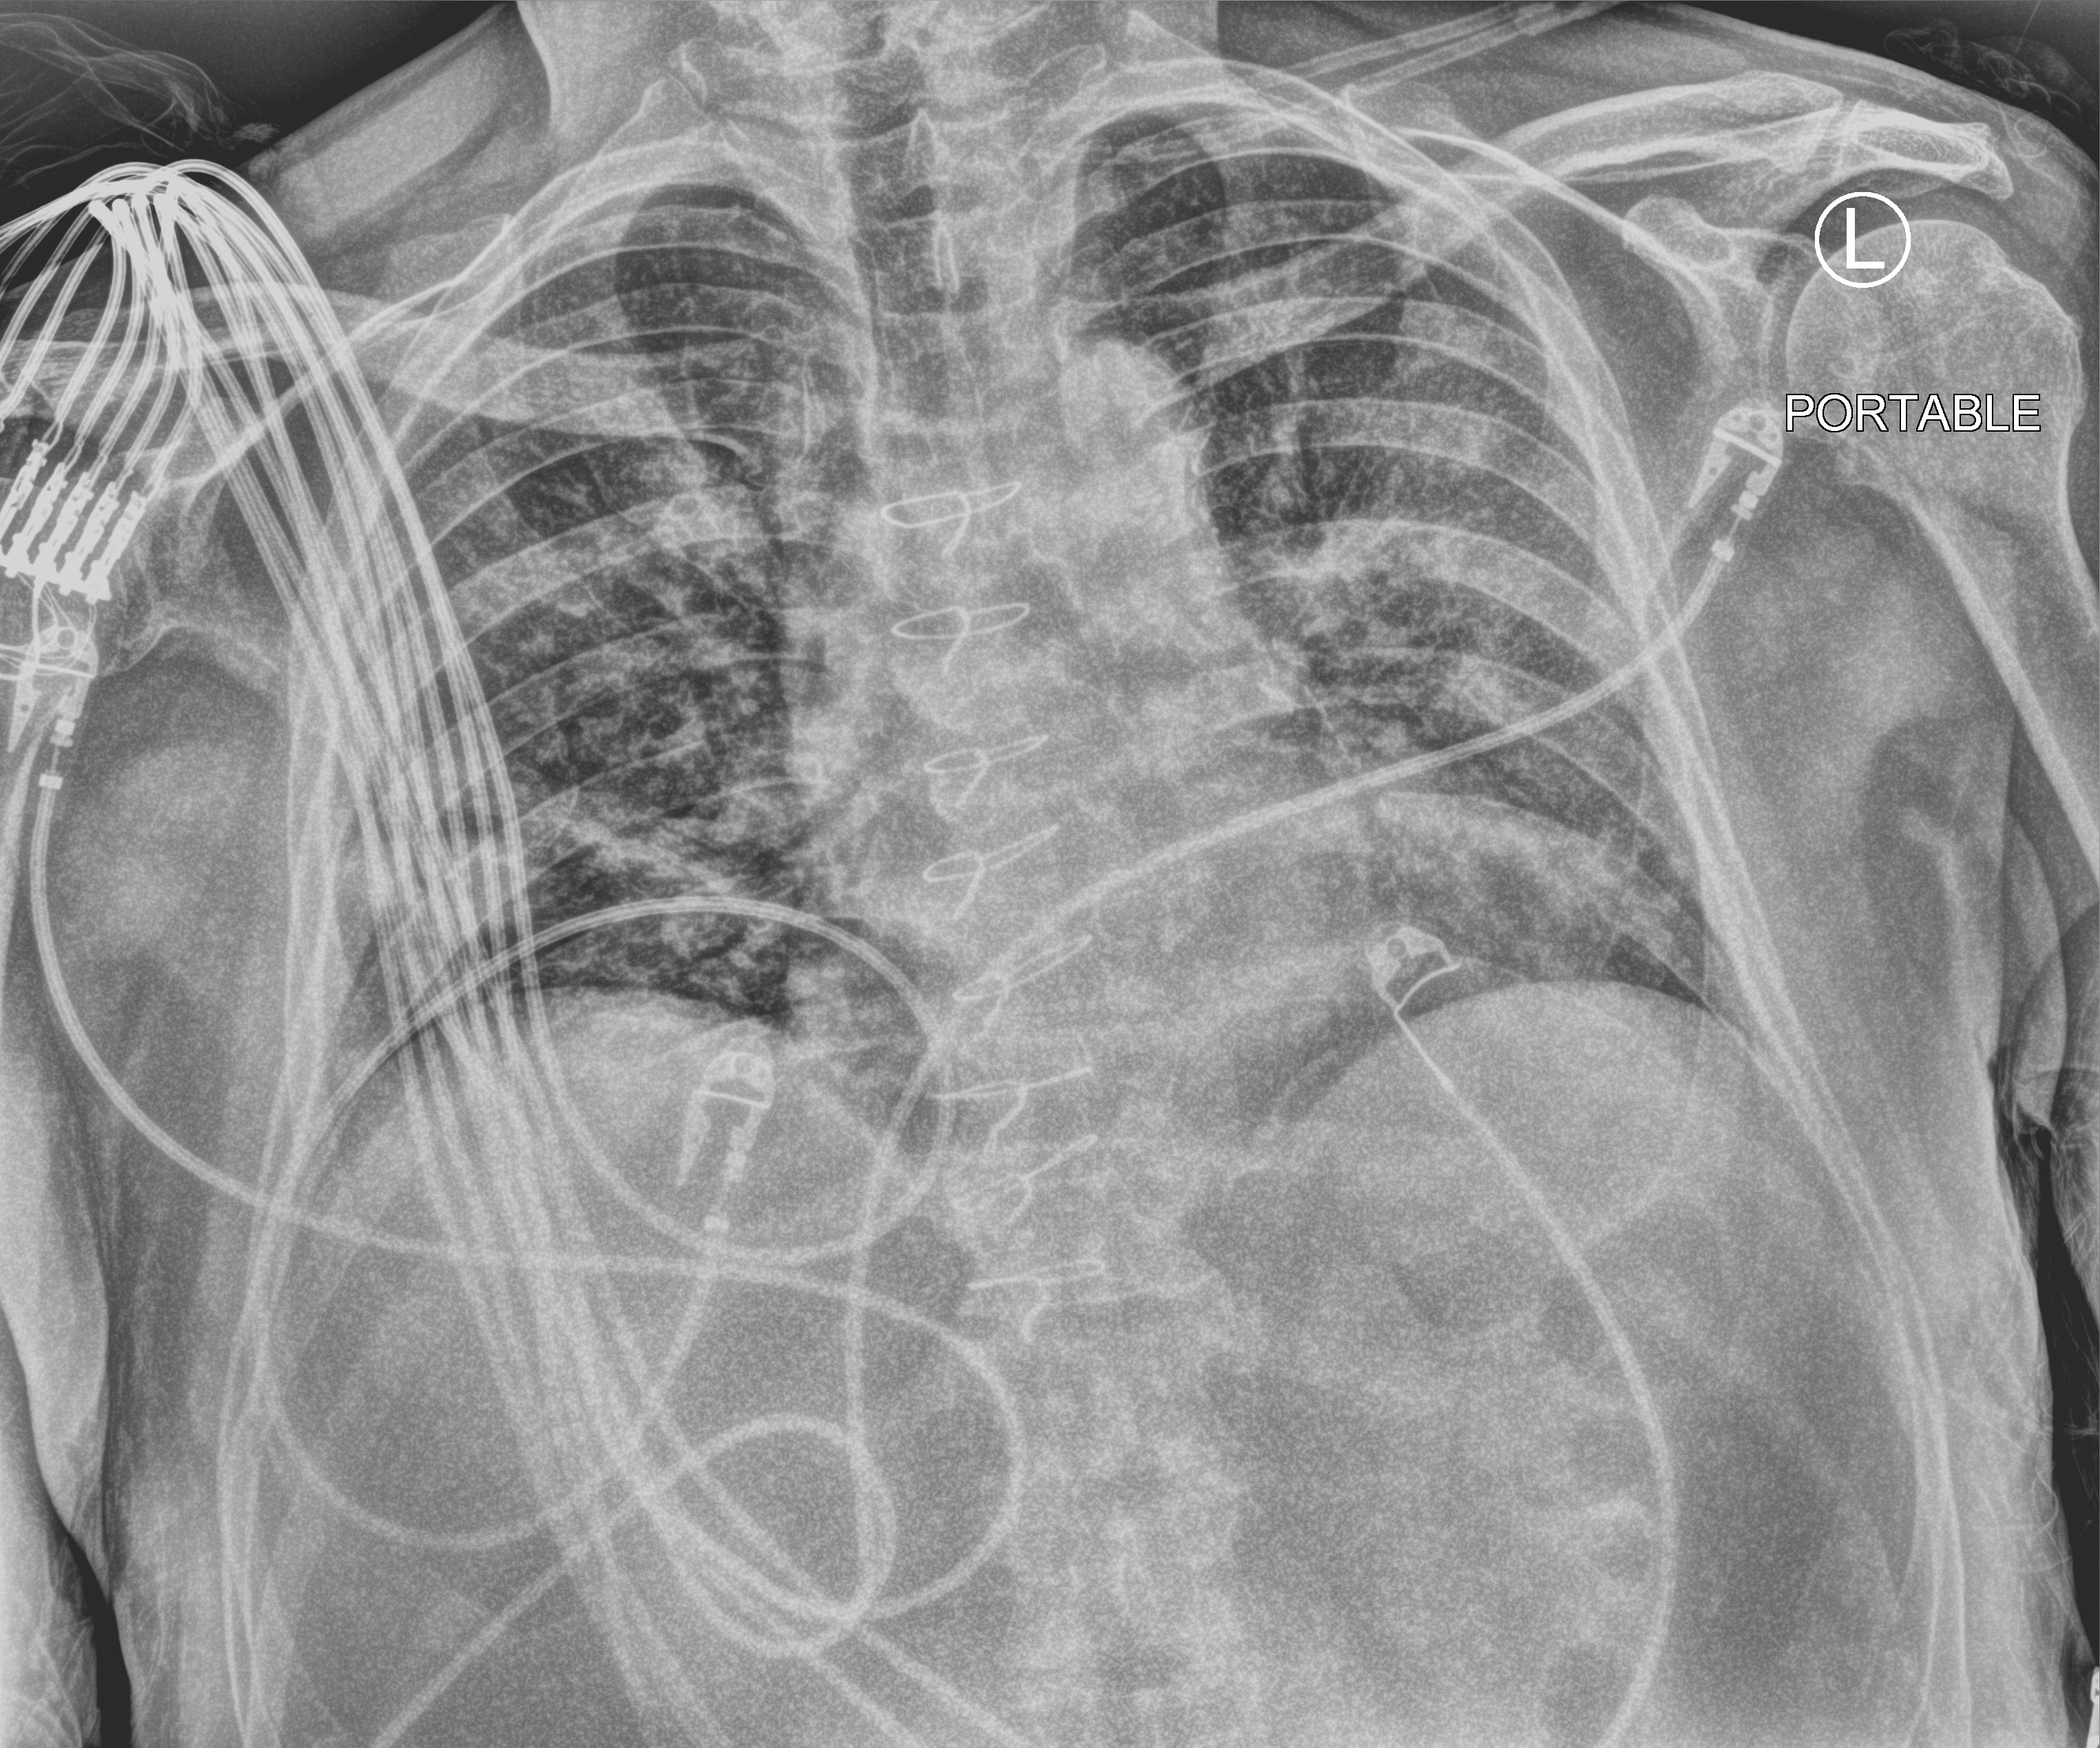
Bedside chest radiograph (computed radiography); anteroposterior (AP) projection. Patient hospitalised with COVID-19; male, aged 60–74 years.
Admission-level facts for this patient (not findings on this image; timing relative to this image not recorded):
- admitted to intensive care during this hospital stay: yes
- length of hospital stay: 22 days